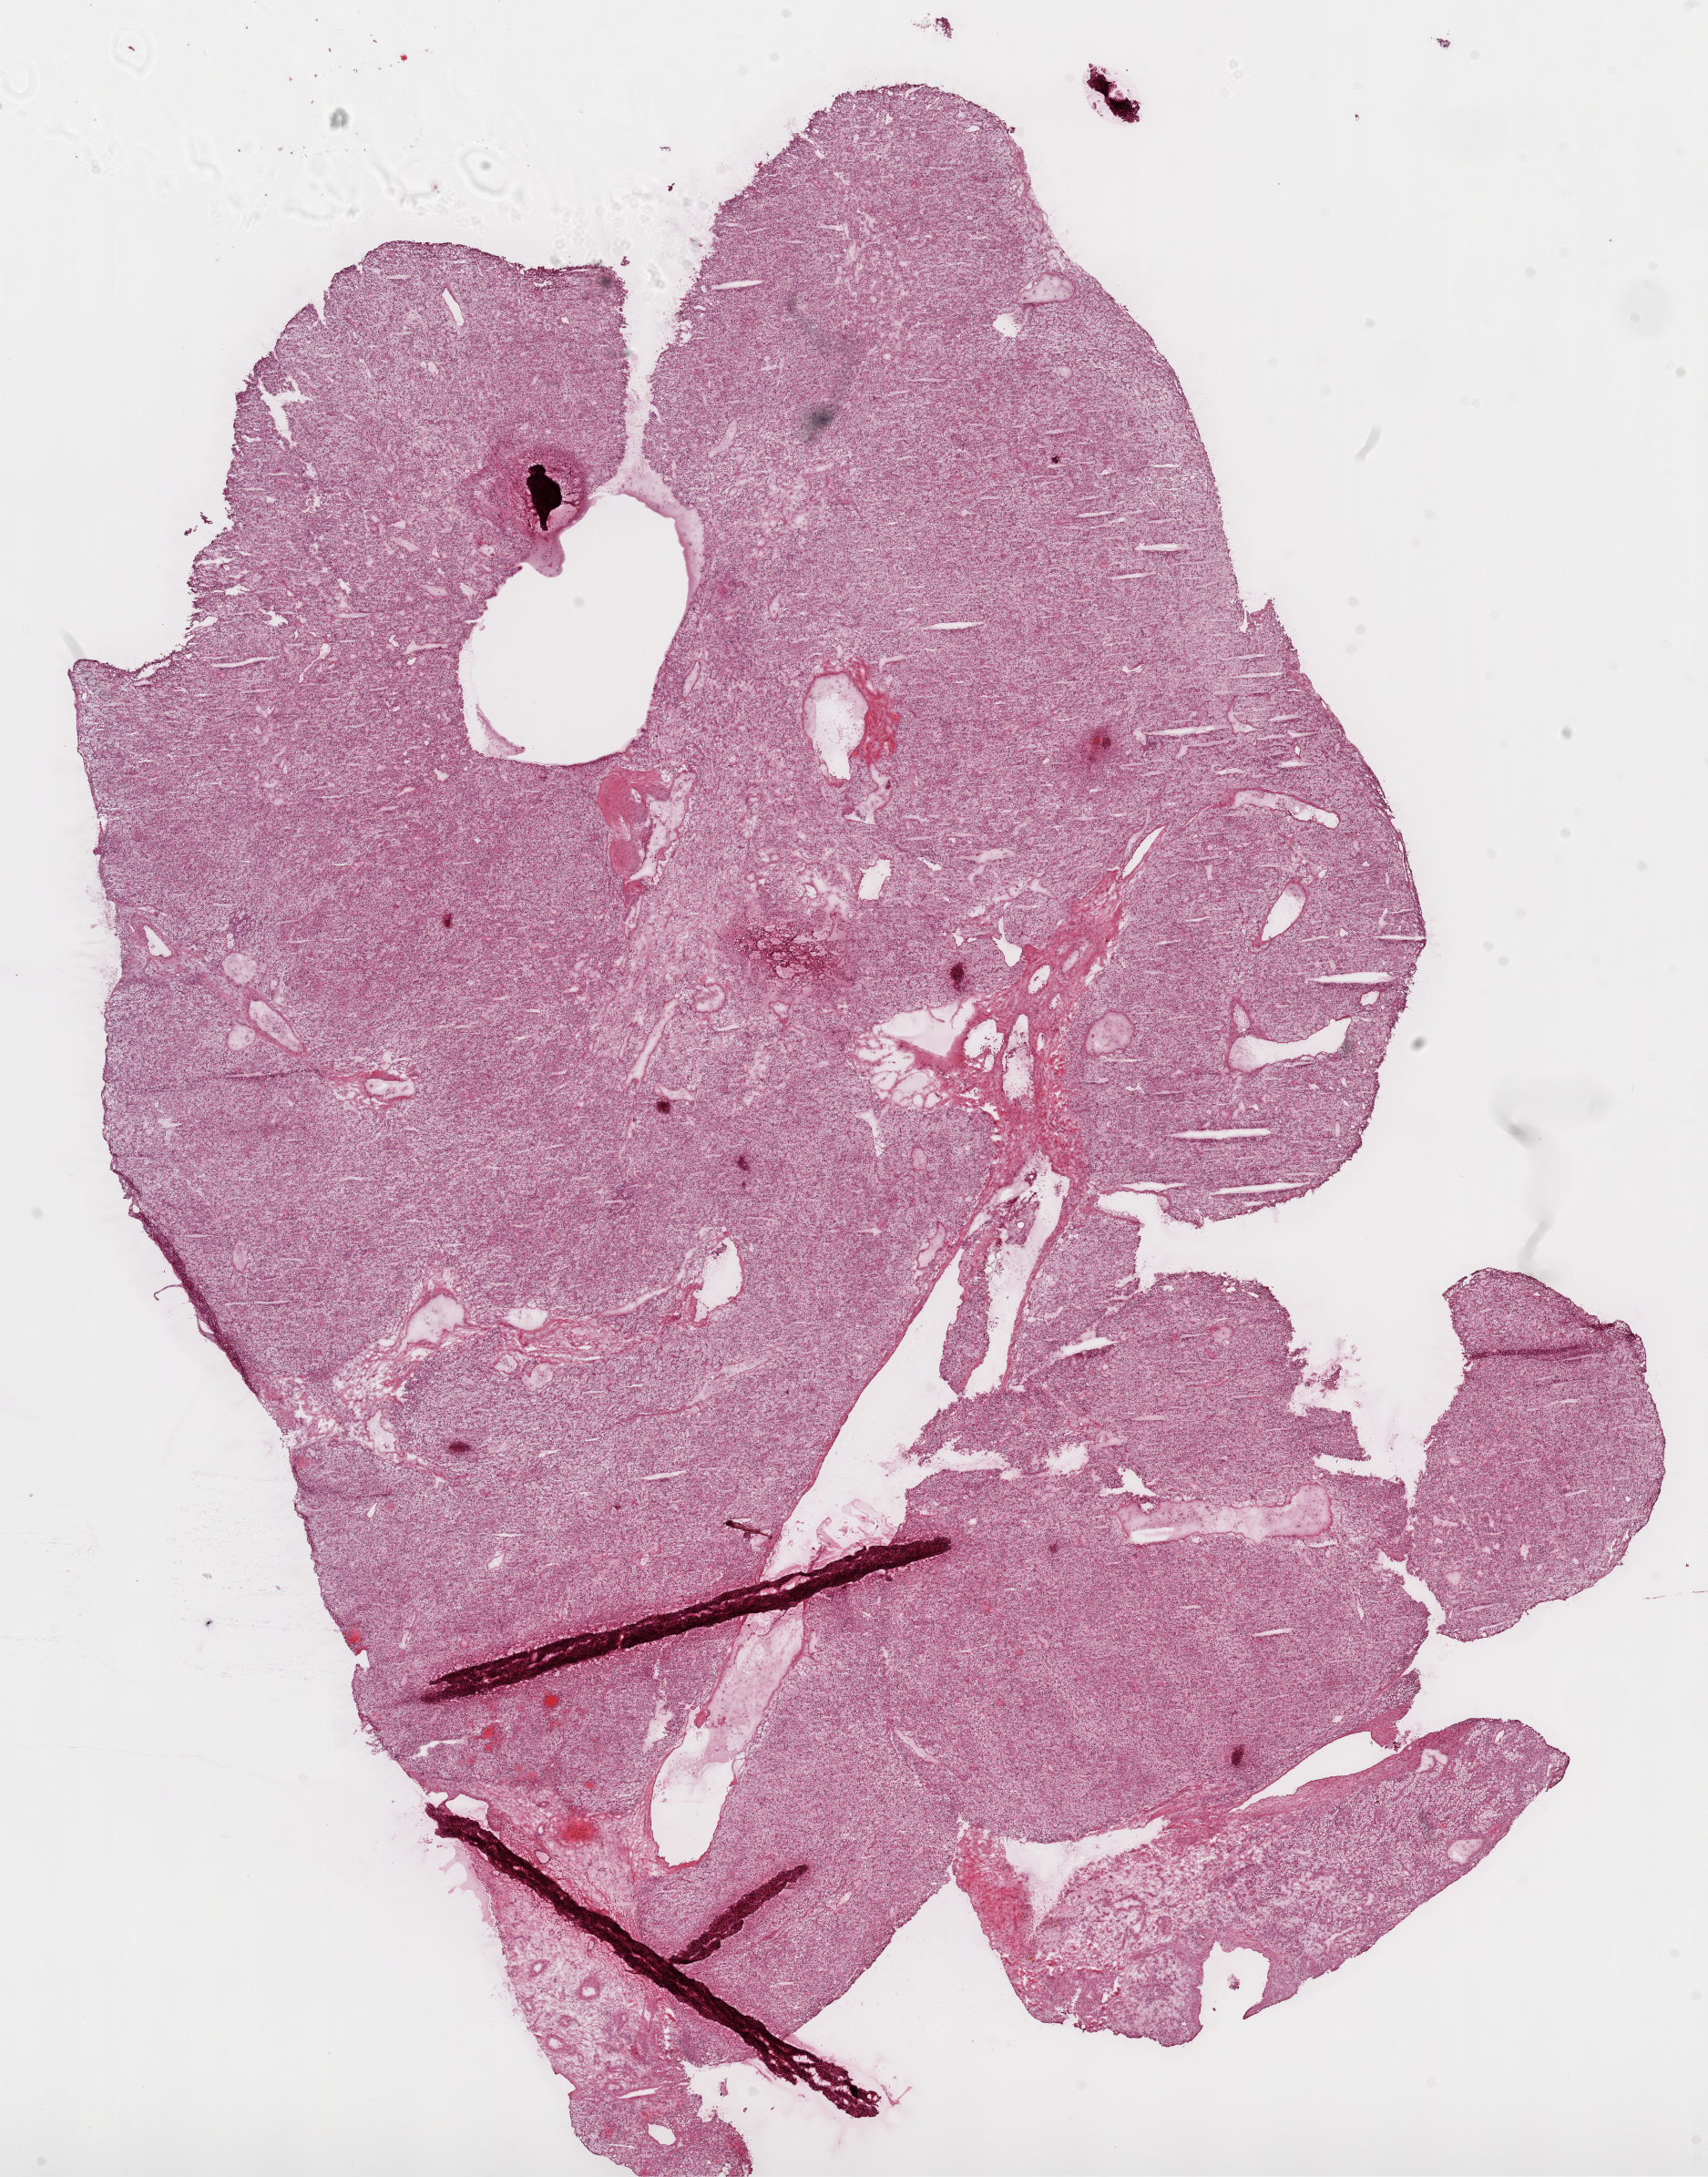
Whole-slide histology image, H&E-stained — low-resolution overview of the scanned area, about 15.0 x 19.2 mm, frozen section from the top of the tissue portion, kidney, primary tumour sample. Female, age 58 years at initial diagnosis.
Diagnosis: Clear cell adenocarcinoma, NOS.